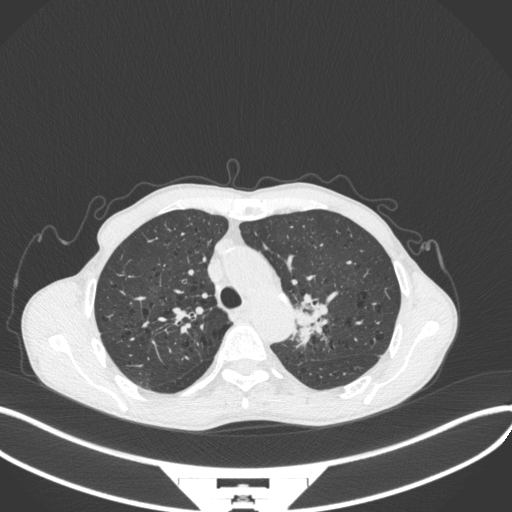
Chest CT, one axial slice; reconstruction kernel B31f; lung window (W 1500 / L -600 HU); 1 mm slice thickness; 512 × 512 image matrix. Male patient, age 65 years. Case-level facts recorded for this patient, not image findings: clinical TNM (as recorded): T2b N0 M0; histopathological grade: G2.
Annotated regions visible in this slice (rectangle marked by the reading radiologist):
- lung tumour (recorded histology: adenocarcinoma): bounding box [x1, y1, x2, y2] px = [292, 286, 333, 355]